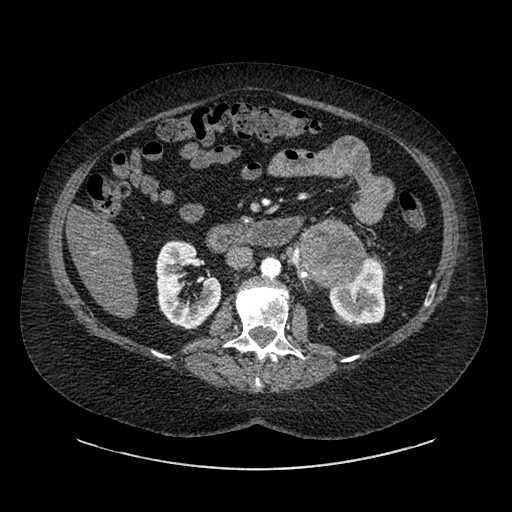
Contrast-enhanced abdominal CT, one axial slice; reconstruction kernel SOFT; intravenous contrast given; soft-tissue window (W 400 / L 40 HU); 0.62 mm slice thickness; 512 × 512 image matrix, field of view 460 × 460 mm. Patient: female, 61 years. Case-level facts recorded for this patient, not image findings: diagnosis: adrenocortical carcinoma; tumour side: left adrenal; tumour size at pathology: 13 cm; Ki-67 index: 79 %; stage (as recorded): 2.
Outlined on this slice (semi-automatically segmented with operator editing):
- mass: box from (x=299, y=226) to (x=364, y=282) px